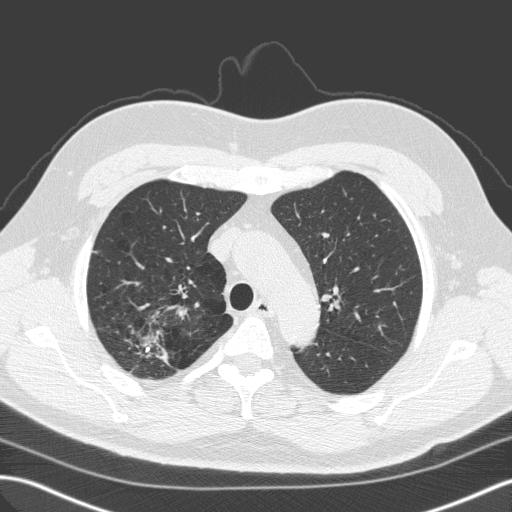
Chest CT (low-dose screening protocol), one axial image. First (baseline) screen. Lung window (W 1500 / L -600 HU). Standard (soft-tissue) reconstruction kernel (C). 120 kVp. Male, age 59 years at enrolment. Former smoker at enrolment.
Expert-annotated lung lesion, bounding box [x1, y1, x2, y2] px = [116, 307, 178, 374]. The exam's reader record, not a measurement of the box and not confirmed to be the same lesion: non-calcified nodule or mass ≥4 mm, right upper lobe, 28 × 25 mm, spiculated (stellate) margins, soft tissue attenuation. Official screen result: positive, change unspecified: nodule(s) >= 4 mm or enlarging nodule(s), mass(es), or other non-specific abnormalities suspicious for lung cancer. Later outcome: lung cancer diagnosed 64 days after this screen — large cell carcinoma, NOS, right upper lobe, undifferentiated (G4), stage IA (AJCC 6th edition), 25 mm at pathology.